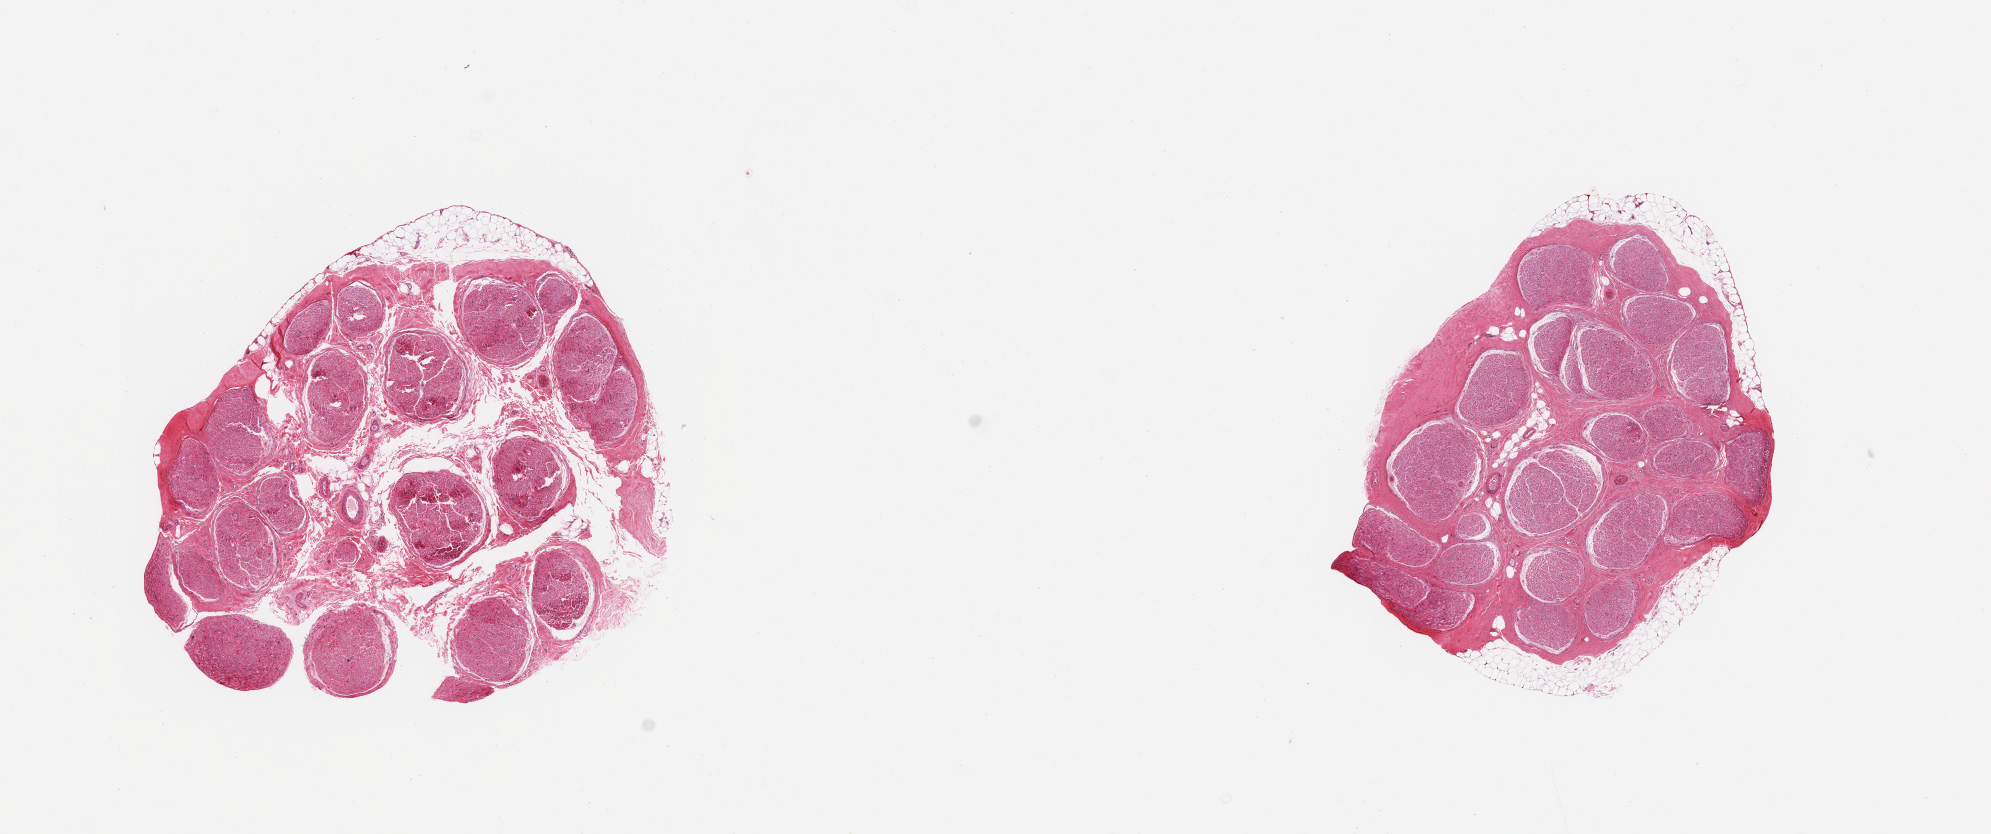
Digitized H&E-stained section, a low-resolution overview of the entire scanned area, about 15.8 x 6.6 mm. PAXgene-fixed paraffin-embedded (PFPE) section. Section of tibial nerve (target tissue). Tissue donor sample. Male donor.
Reviewer comment on this tissue sample: 2 pieces, trace adherent nubbins of adherent fat, up to ~0.4mm.